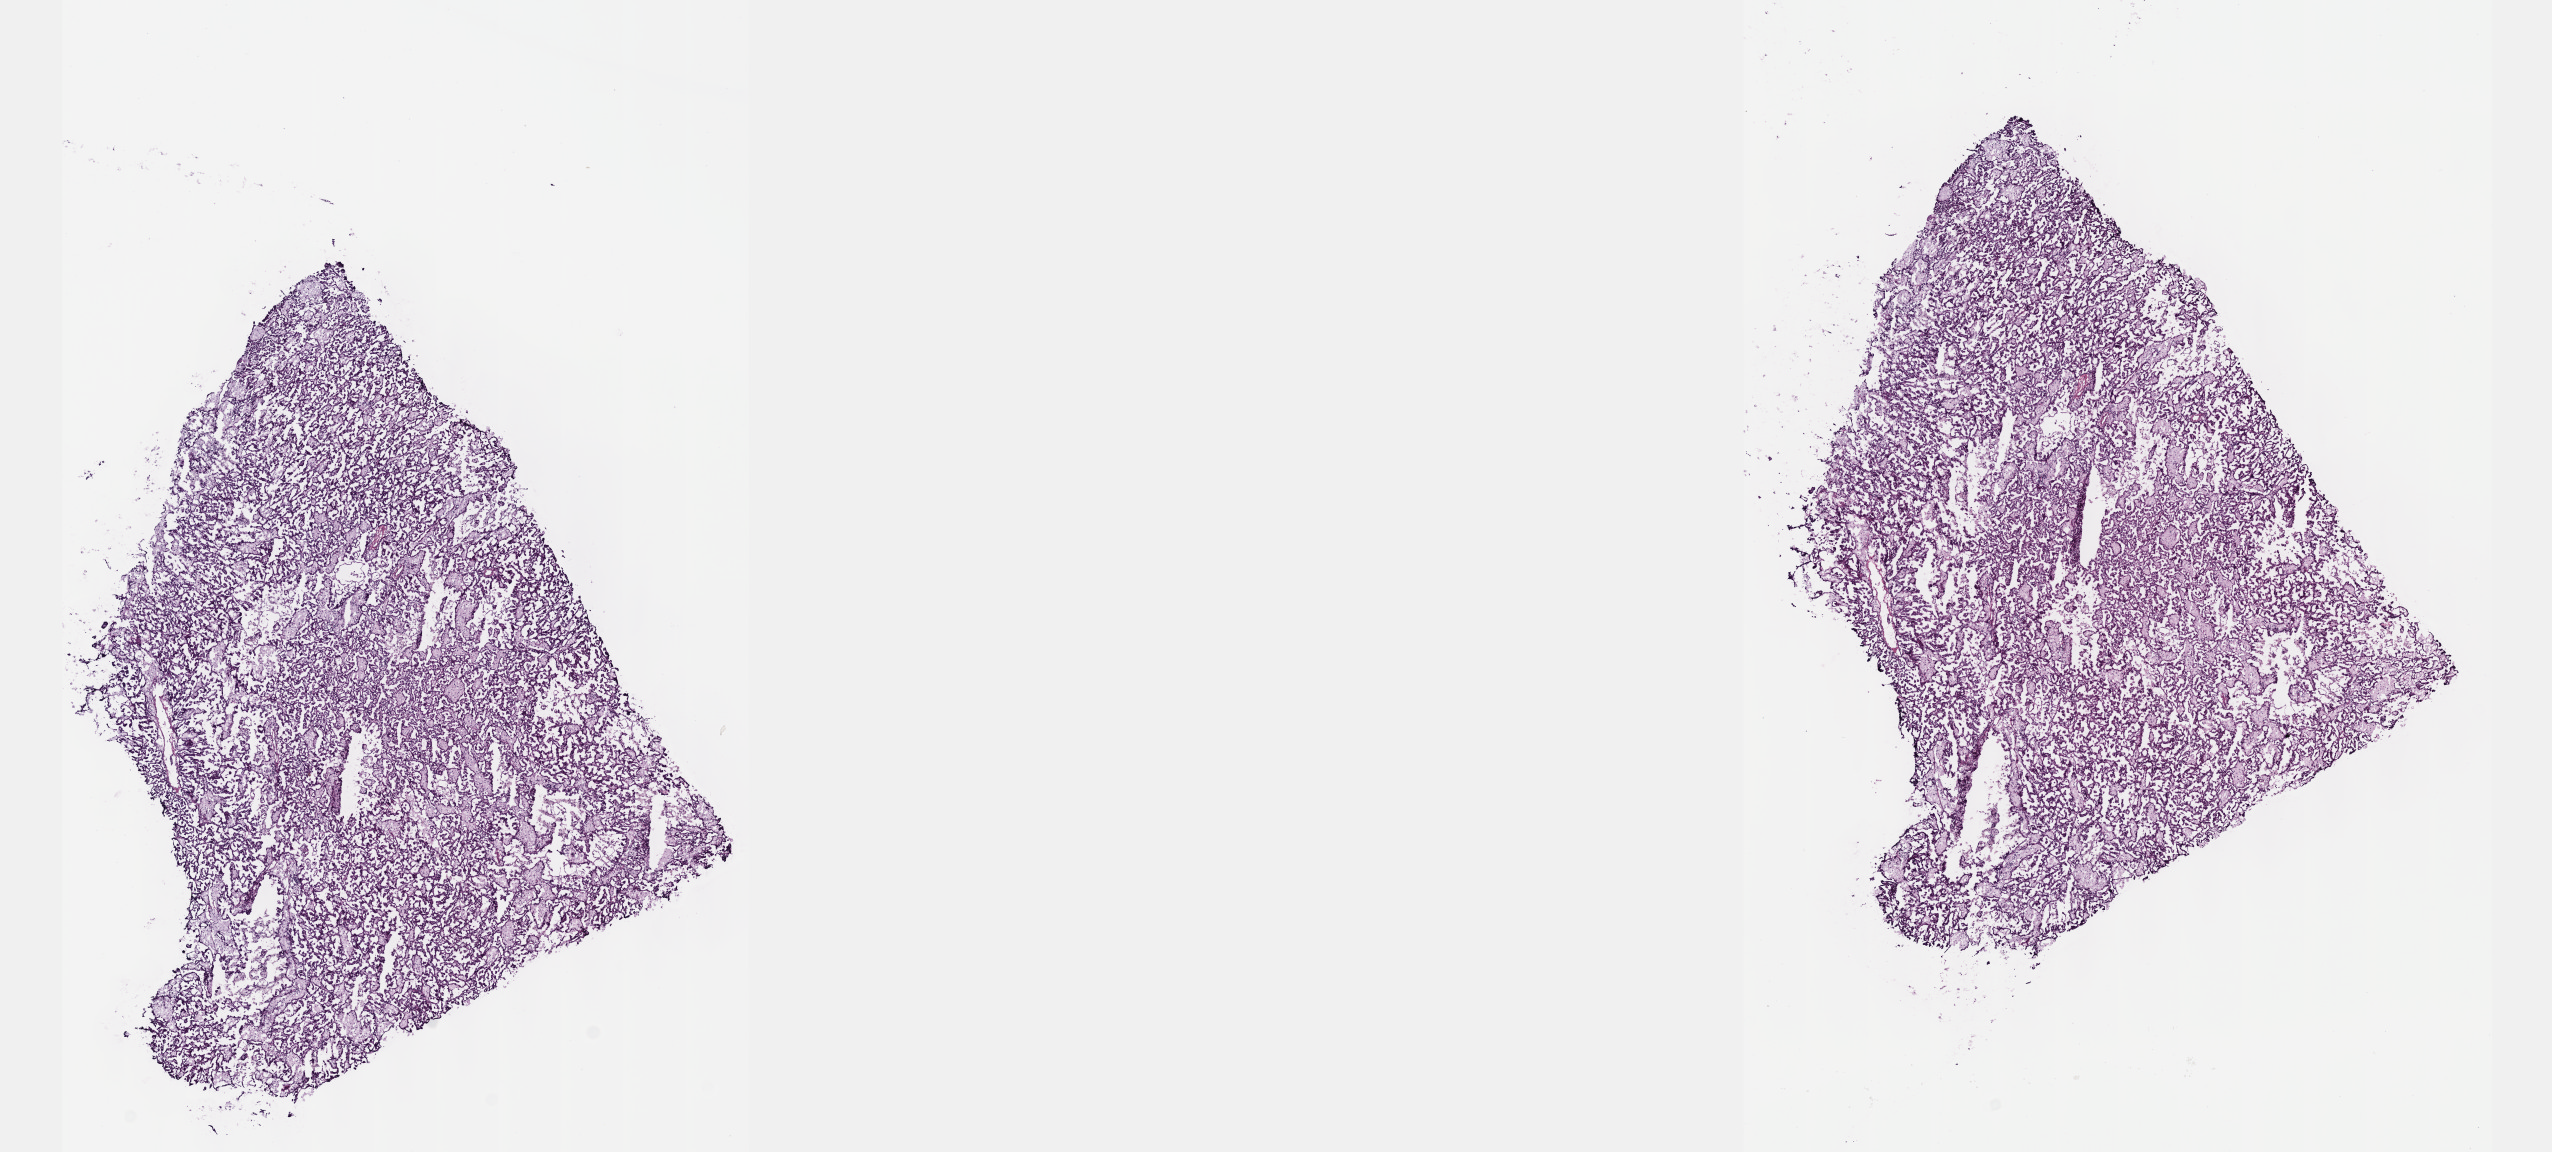
Digitized H&E-stained tissue section (whole slide), a low-resolution overview of the entire scanned area, about 20.6 x 9.3 mm (acquisition: 40x scan), frozen section from the top of the tissue portion, primary tumour sample from the kidney. Patient: male, age at initial diagnosis 70 years. Composition of this section per pathologist review: tumour cells 65%, tumour nuclei 85%.
Diagnosis: Papillary adenocarcinoma, NOS.